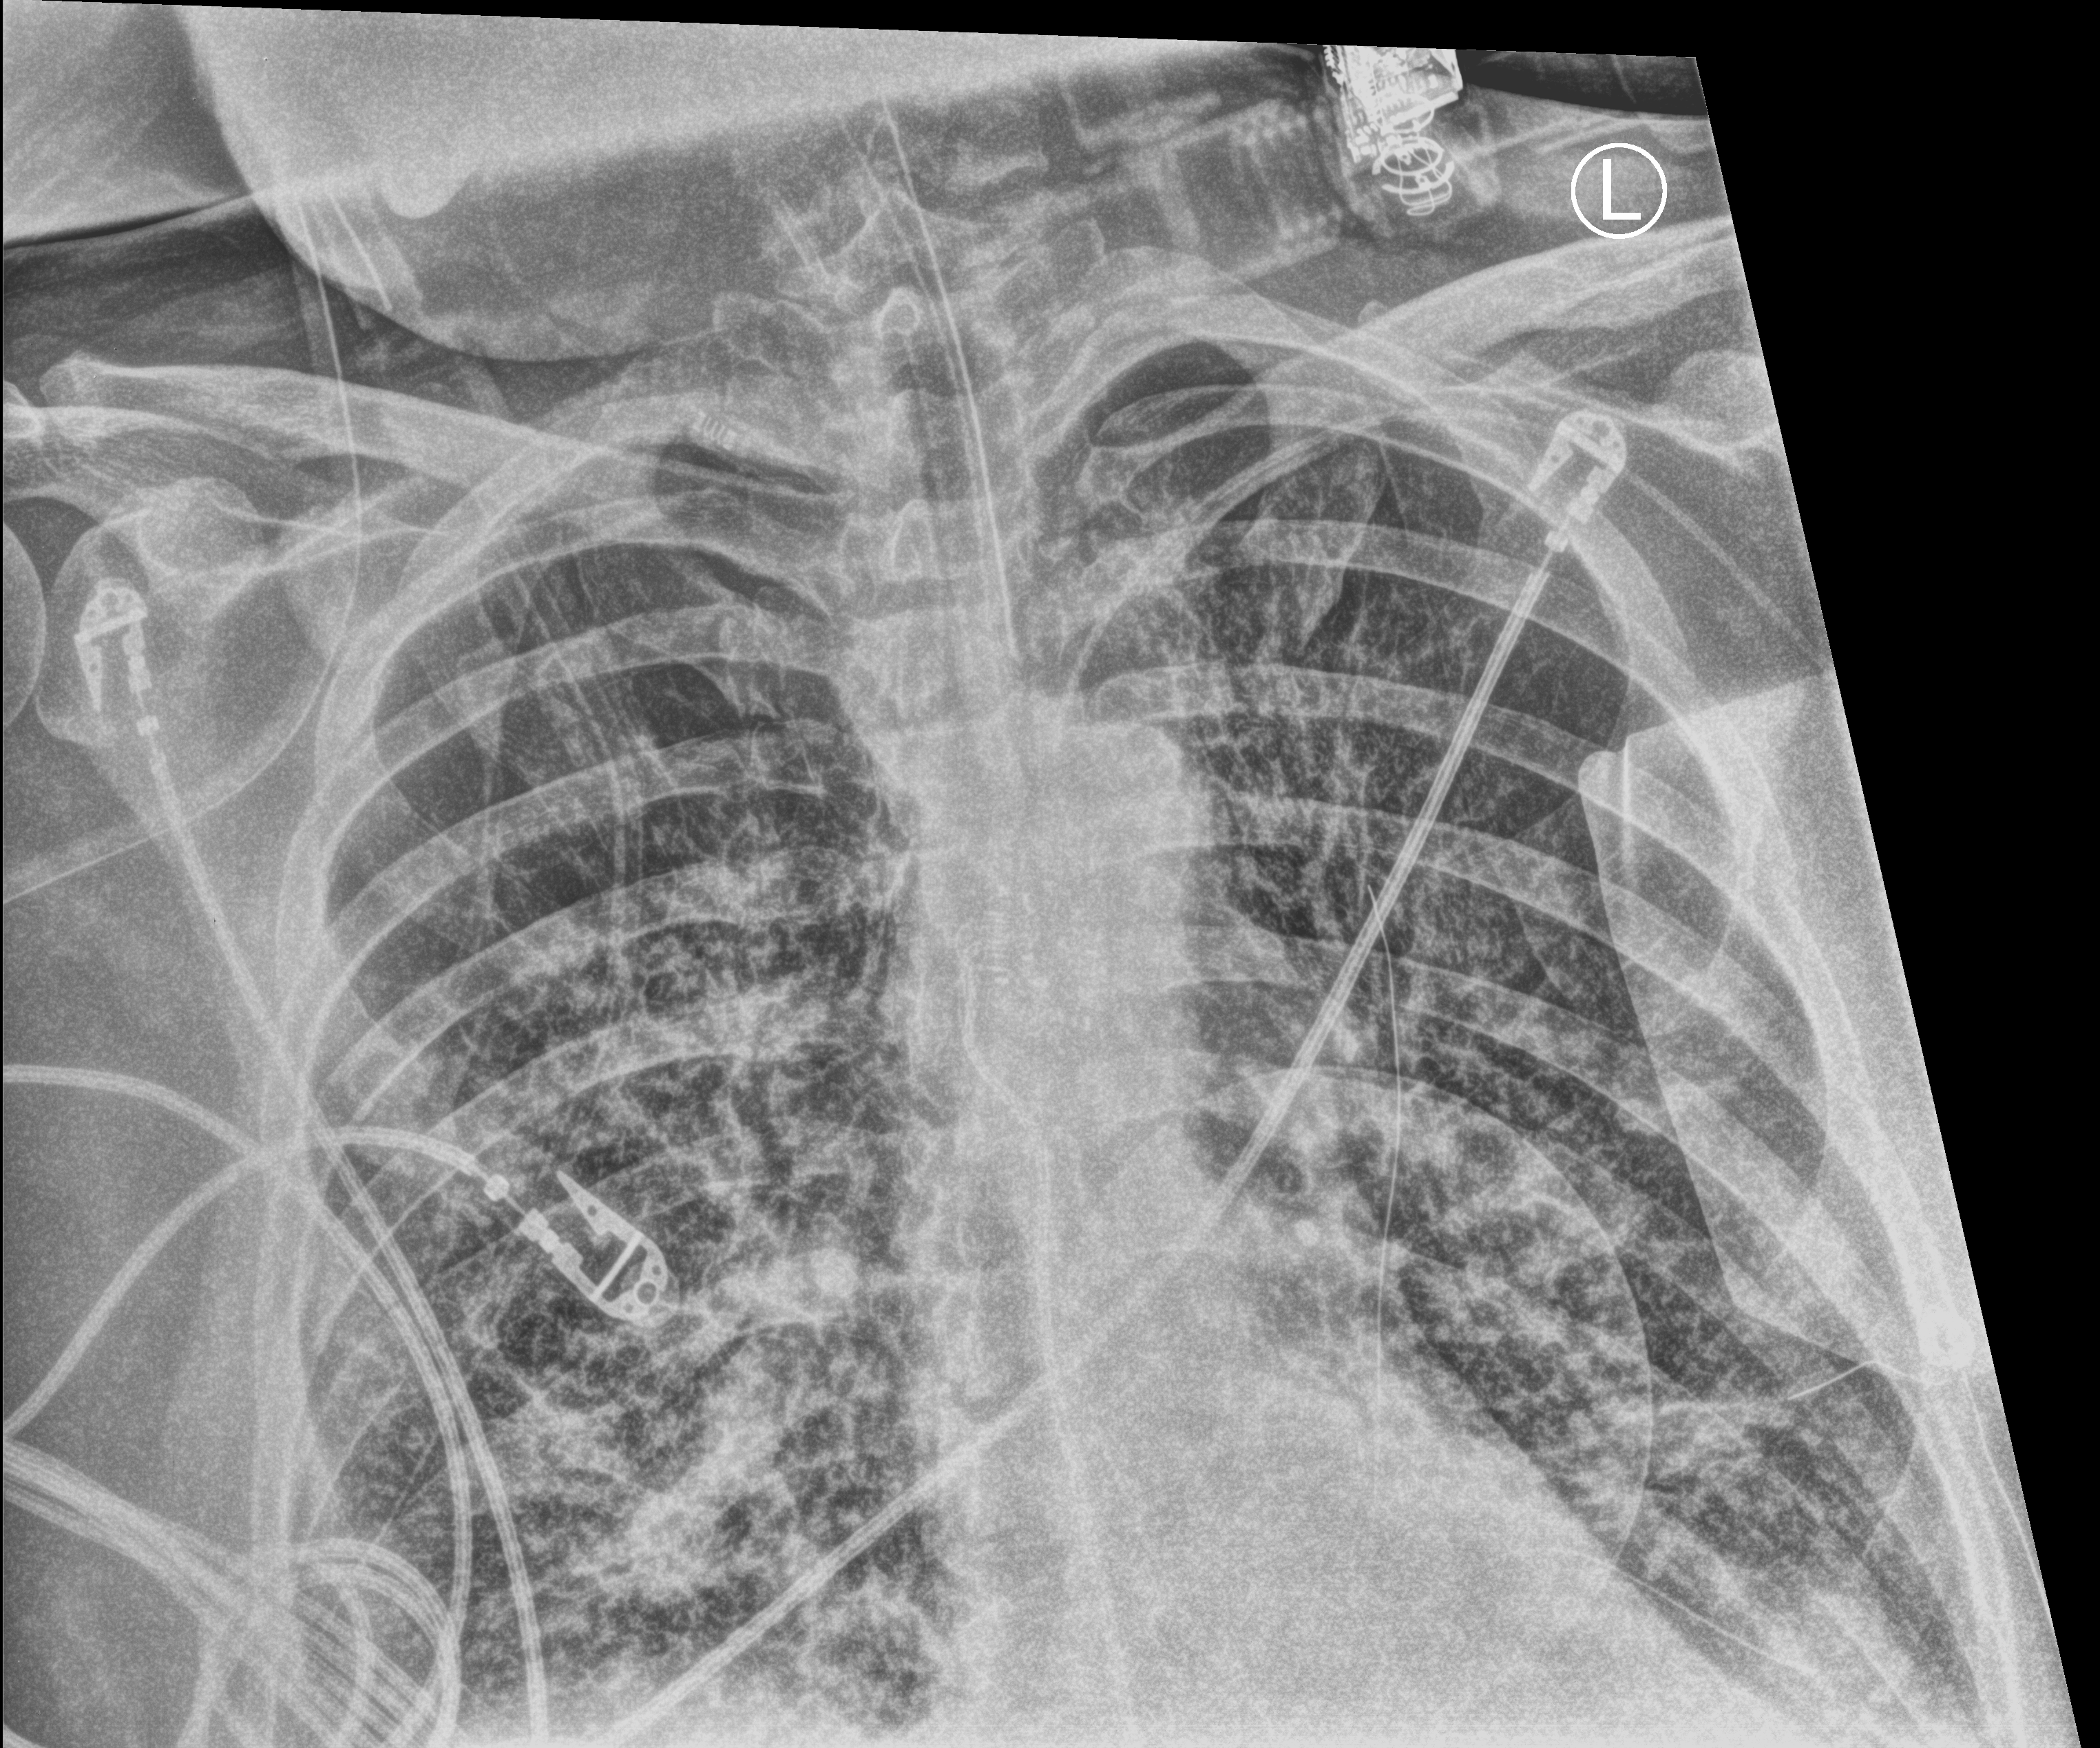
Portable chest radiograph, anteroposterior (AP) projection. Patient hospitalised with COVID-19, aged 18–59 years.
Admission-level facts for this patient (not findings on this image; timing relative to this image not recorded): diabetes (admission record): no; mechanically ventilated during this hospital stay: yes.